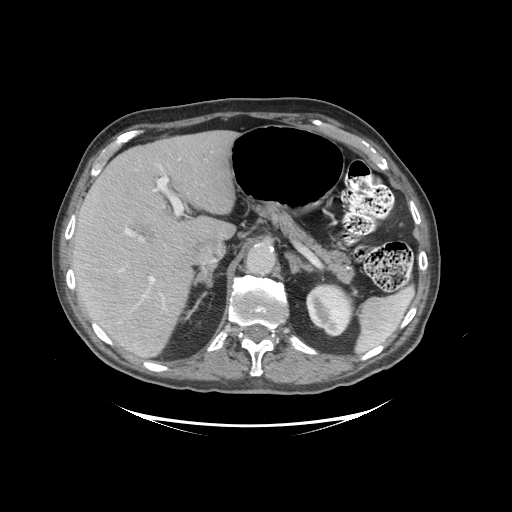
Contrast-enhanced abdominal CT (liver protocol), one axial slice; position 65 of 99 along the scan axis; 140 kVp; soft-tissue window (W 400 / L 40 HU); 2.5 mm slice thickness; 512 × 512 image matrix, field of view 460 × 460 mm. Case-level facts recorded for this patient, not image findings: diagnosis: hepatocellular carcinoma (patient treated with transarterial chemoembolisation; whether this scan precedes or follows treatment is not stated here); TNM stage (as recorded): Stage-I; Child-Pugh class: A.
Annotated regions visible in this slice (semi-automatic segmentation, software-assisted and operator-edited):
- liver parenchyma outside the tumour (the mass and vessels are separate outlines, so this box may not span the whole liver): box from (x=72, y=130) to (x=236, y=356) px
- liver vessels: (x=121, y=176)–(x=171, y=306)